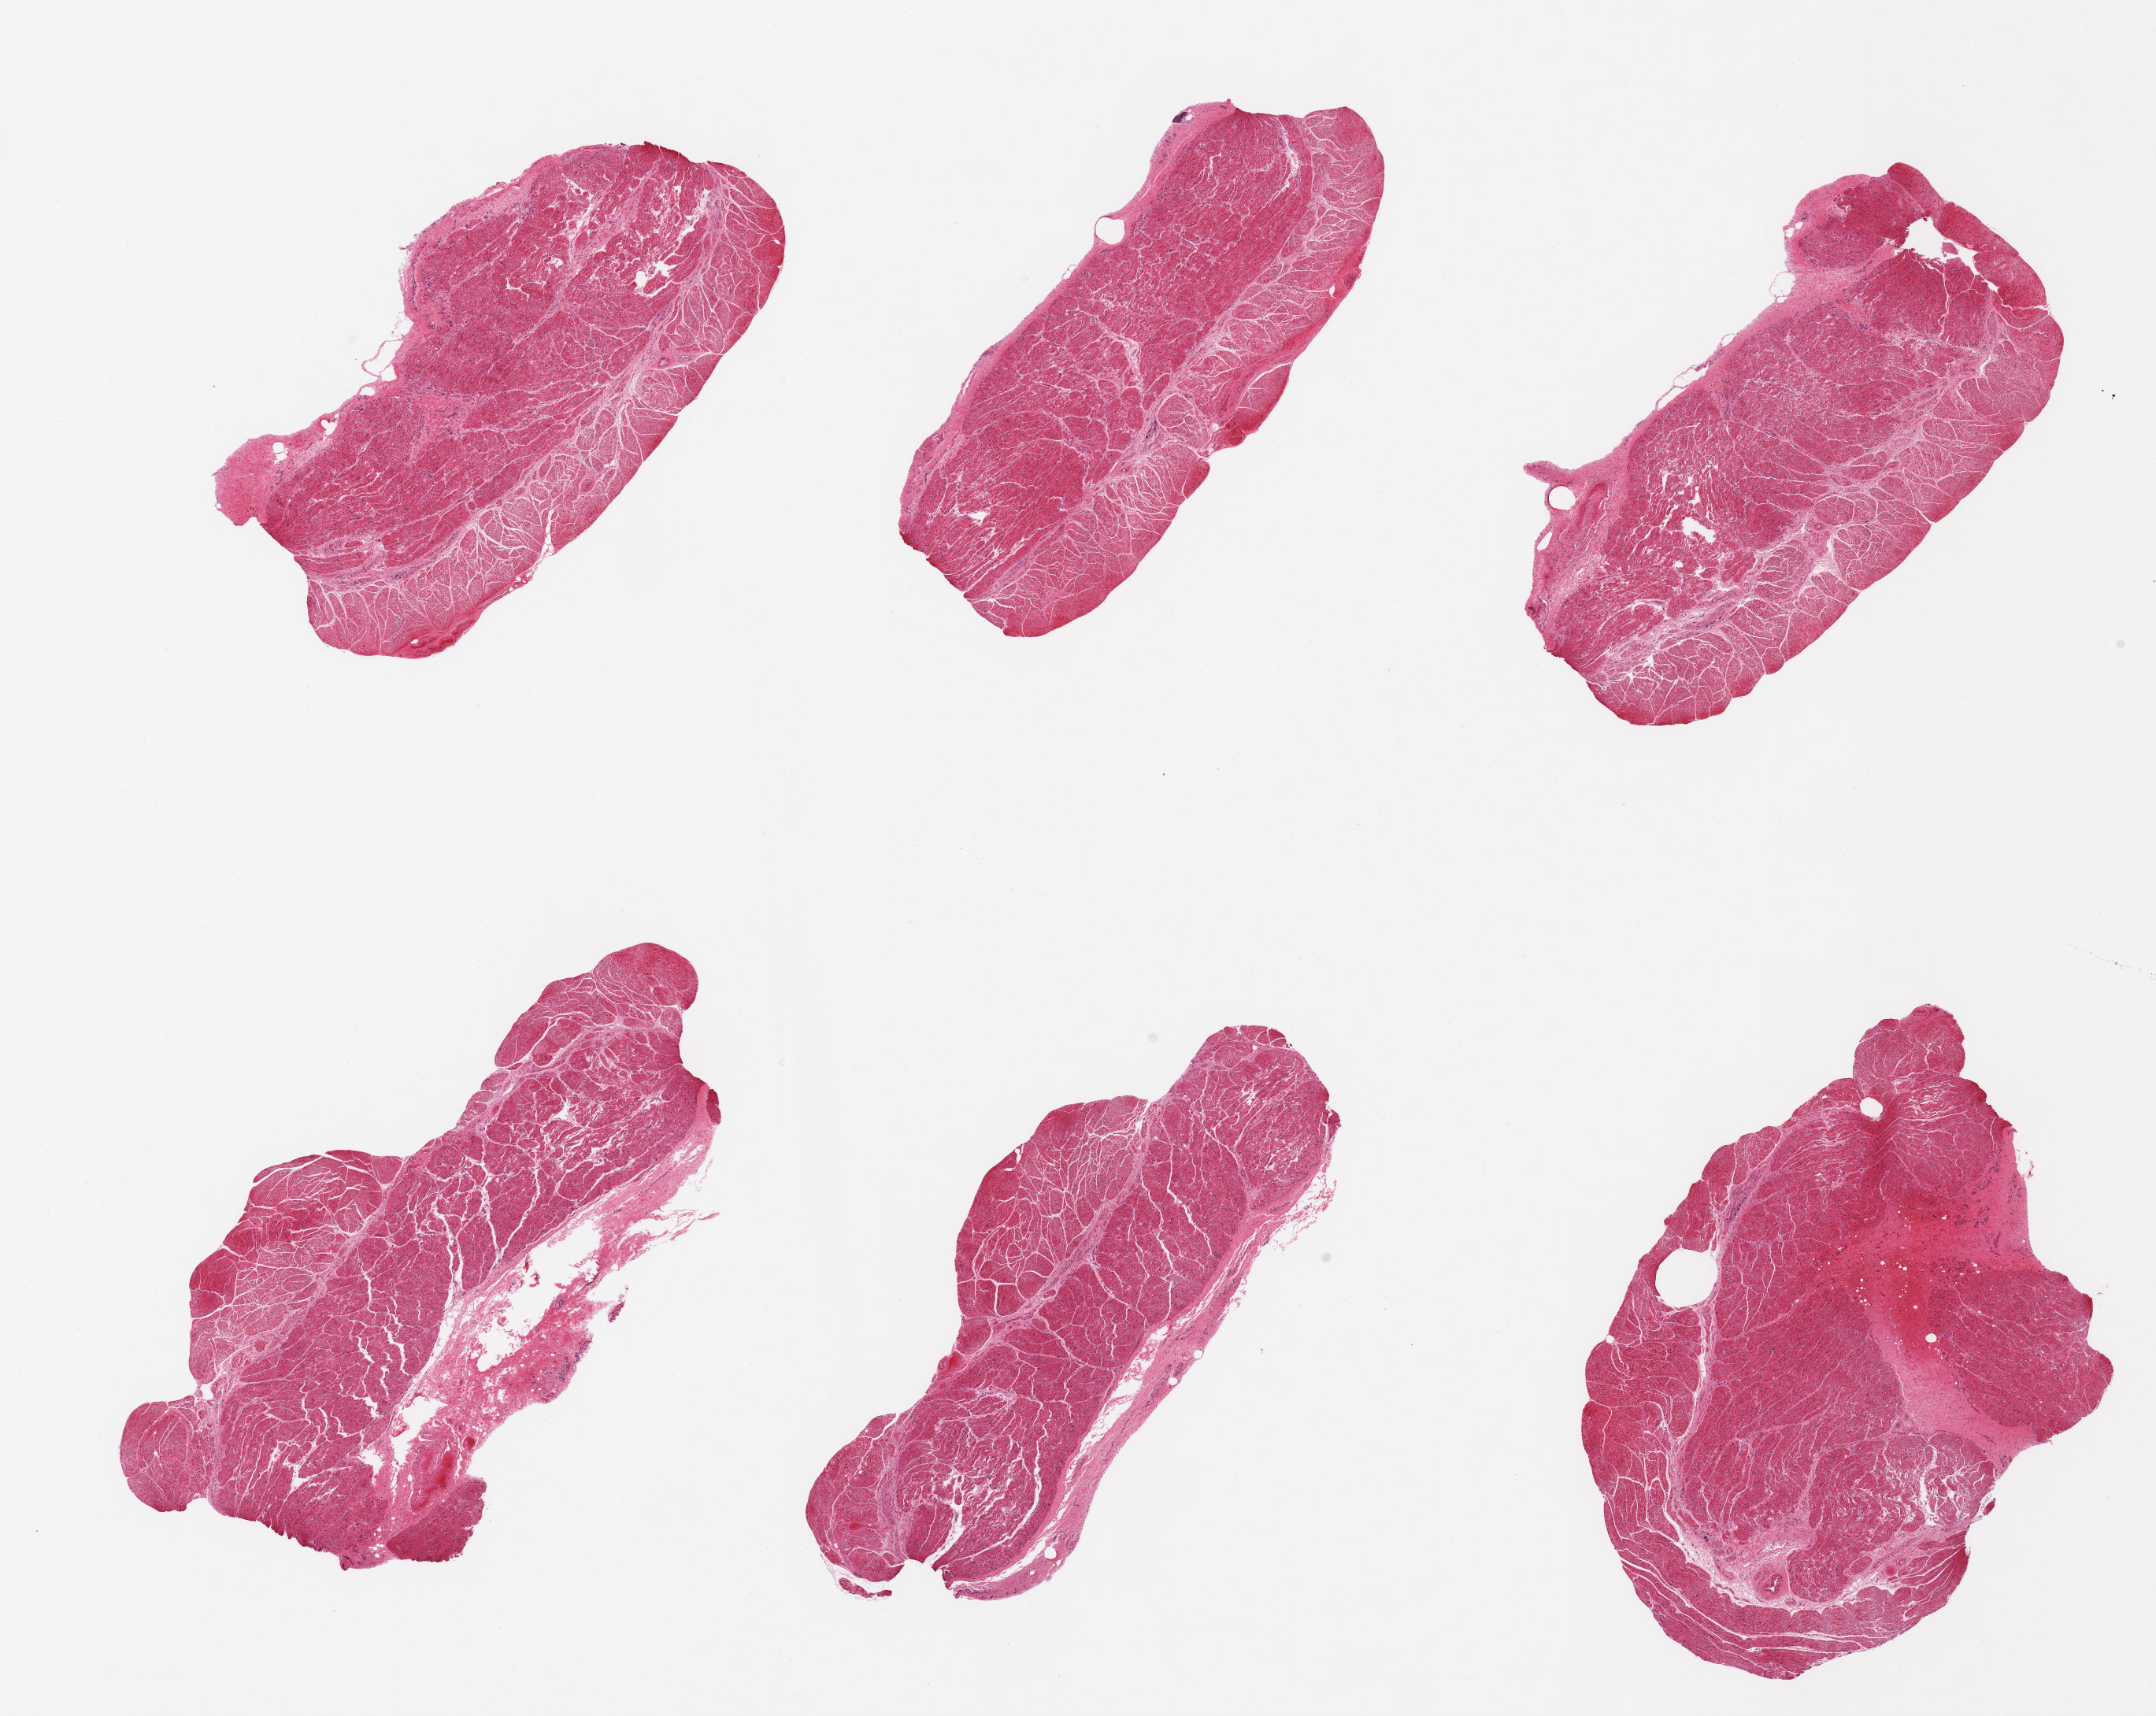
Hematoxylin and eosin (H&E) whole-slide image, shown as a low-resolution overview of the whole scanned area (about 21.7 x 17.2 mm, slide scanned at 20x); PAXgene-fixed paraffin-embedded (PFPE) section; target tissue: esophageal muscle; donor tissue sample. Male donor.
Review note (as recorded): 6 pieces, confirmed target muscularis.